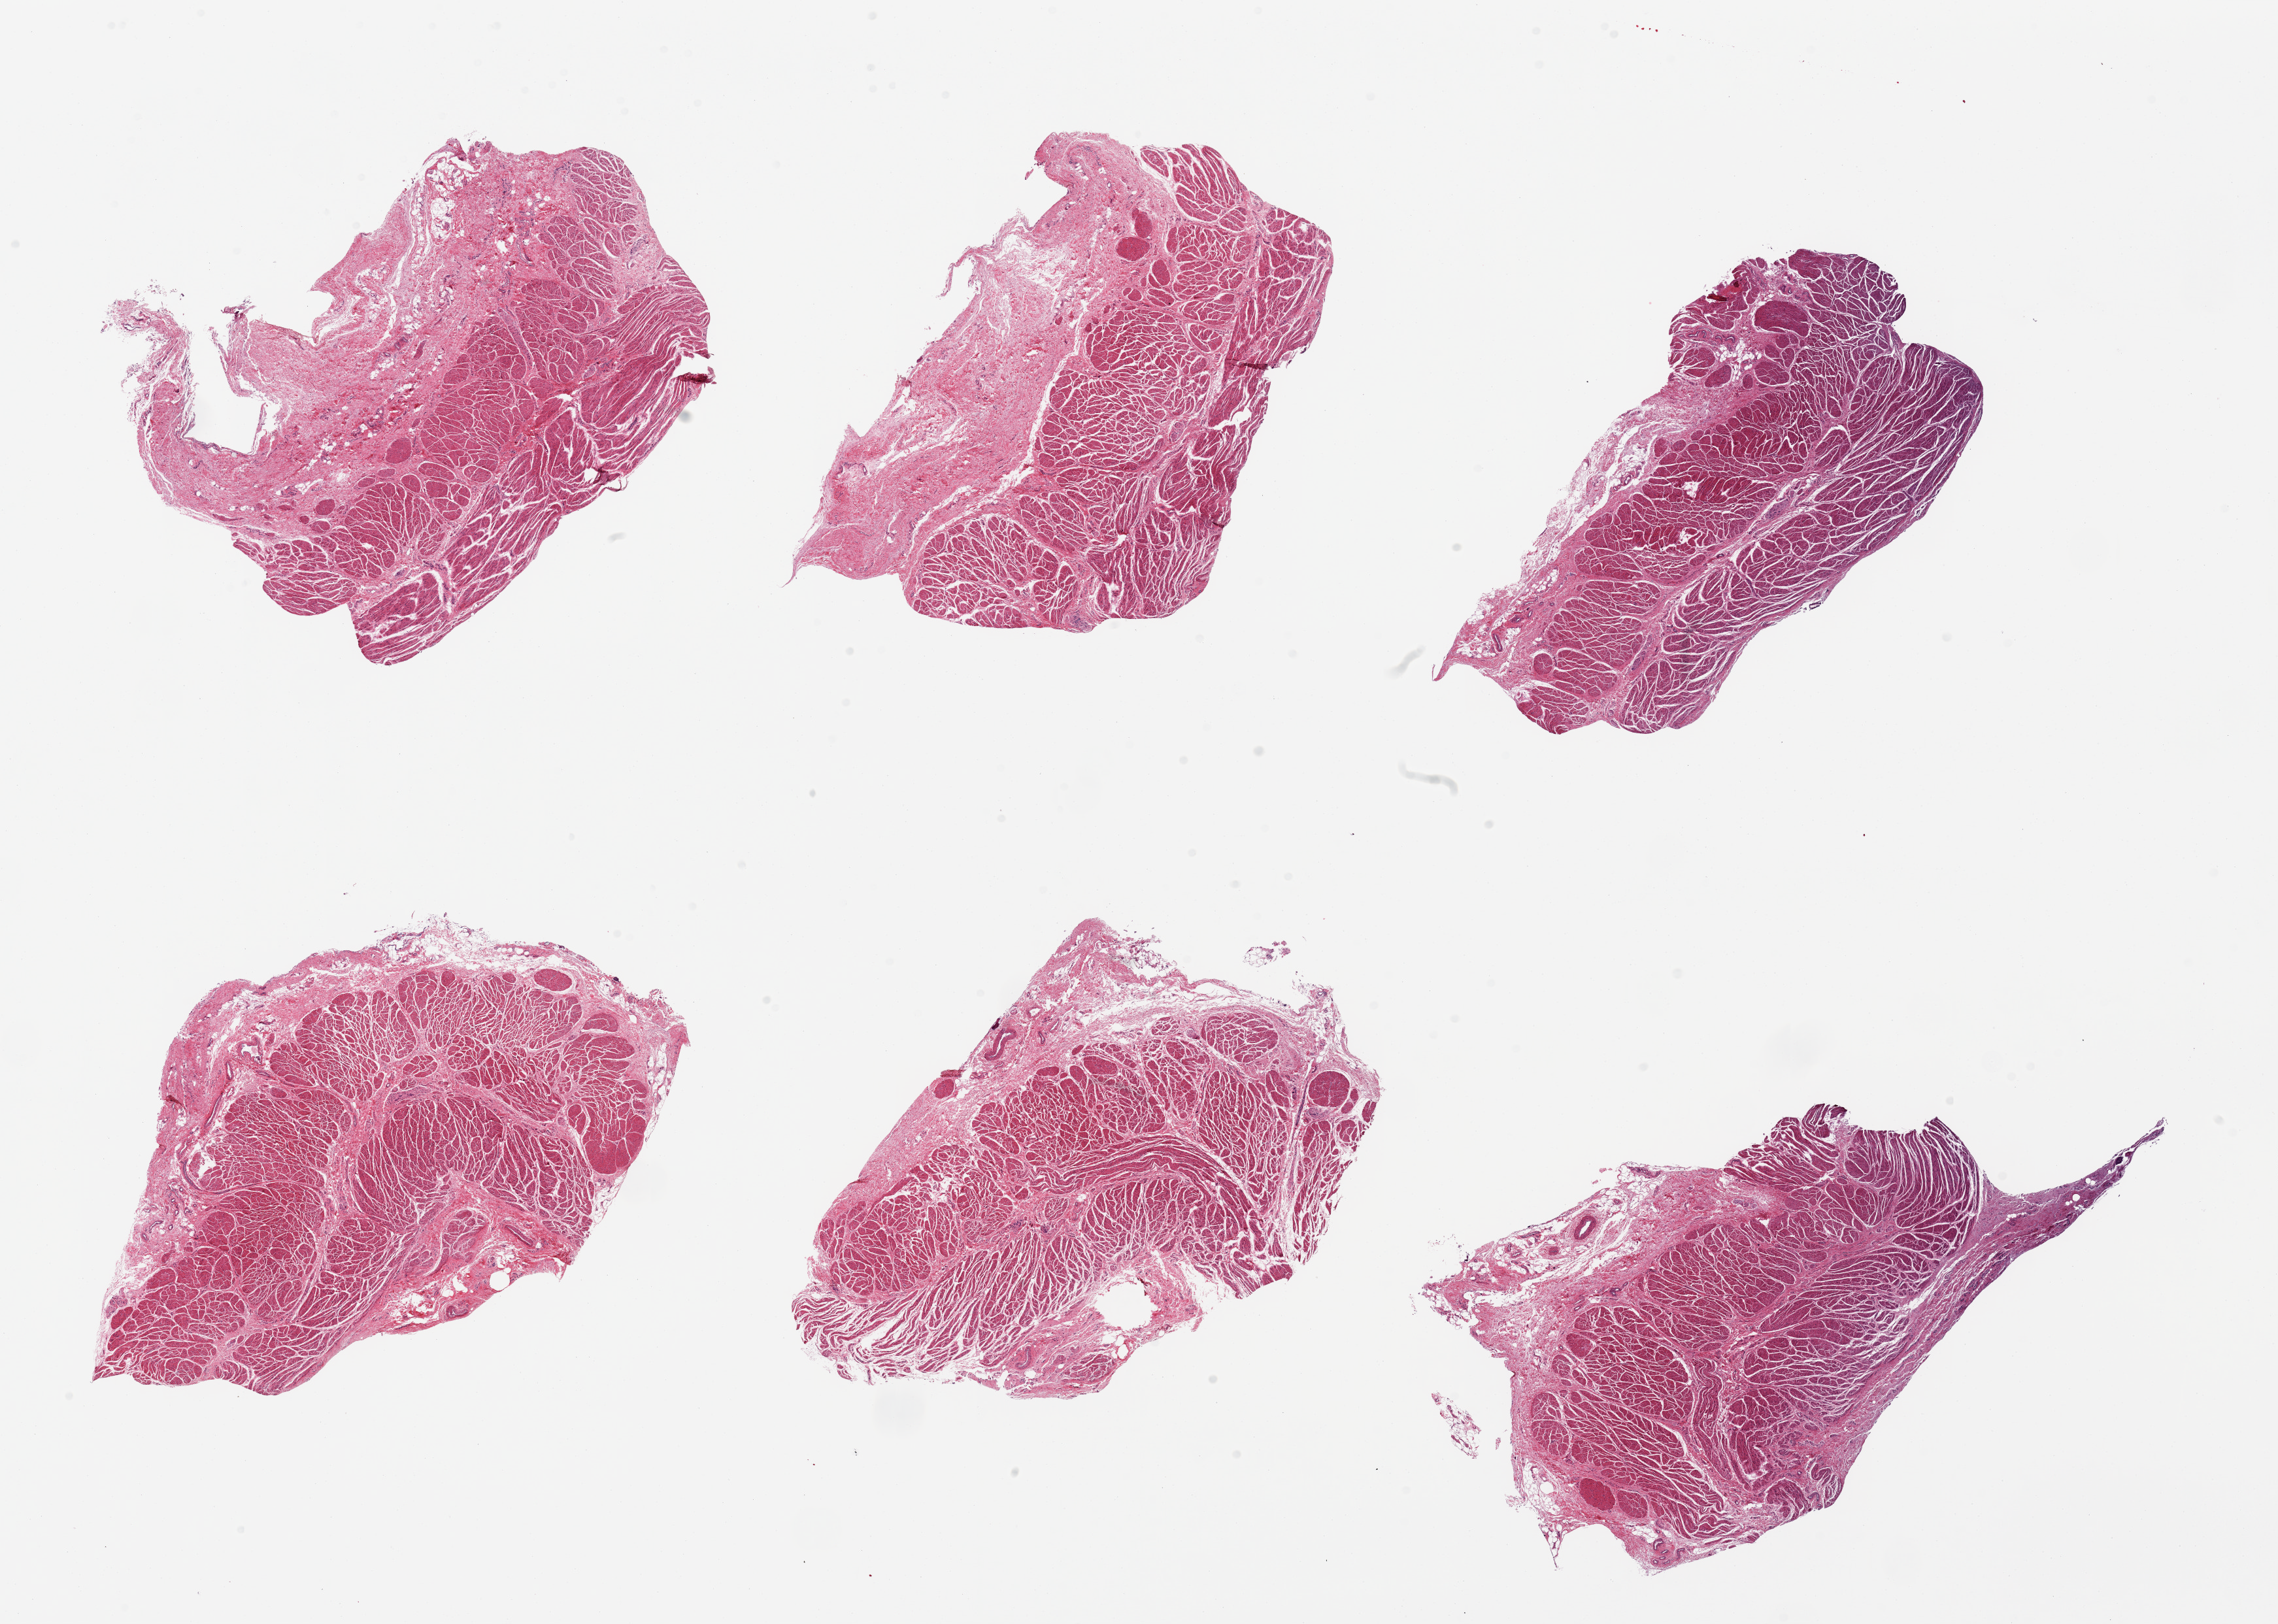
Whole-slide image, hematoxylin and eosin (H&E) stain — low-resolution overview of the scanned area, about 27.6 x 19.7 mm (acquisition: 20x scan). PAXgene-fixed paraffin-embedded (PFPE) section. Section of gastroesophageal junction (target tissue). Tissue donor sample. Male donor.
Pathologist's review note for this sample: 6 pieces; up to 30% submucosa.